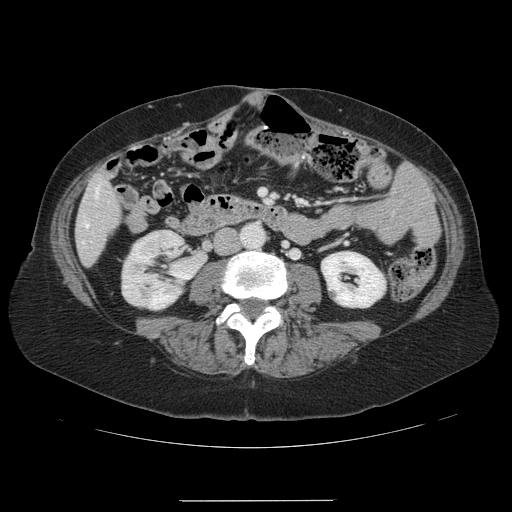
Contrast-enhanced abdominal CT, one axial slice; 120 kVp; intravenous contrast given; soft-tissue window (W 400 / L 40 HU); 2.5 mm slice thickness; 512 × 512 image matrix, field of view 393 × 393 mm. Female patient, age 74 years. Case-level facts recorded for this patient, not image findings: diagnosis: colorectal cancer liver metastases, imaged before liver resection.
Structures marked on this image (expert manual segmentation):
- hepatic veins: box from (x=86, y=187) to (x=98, y=226) px
- liver: (x=76, y=176)–(x=120, y=265)
- planned liver remnant (the part of the liver to remain after resection): (x=76, y=176)–(x=102, y=265)